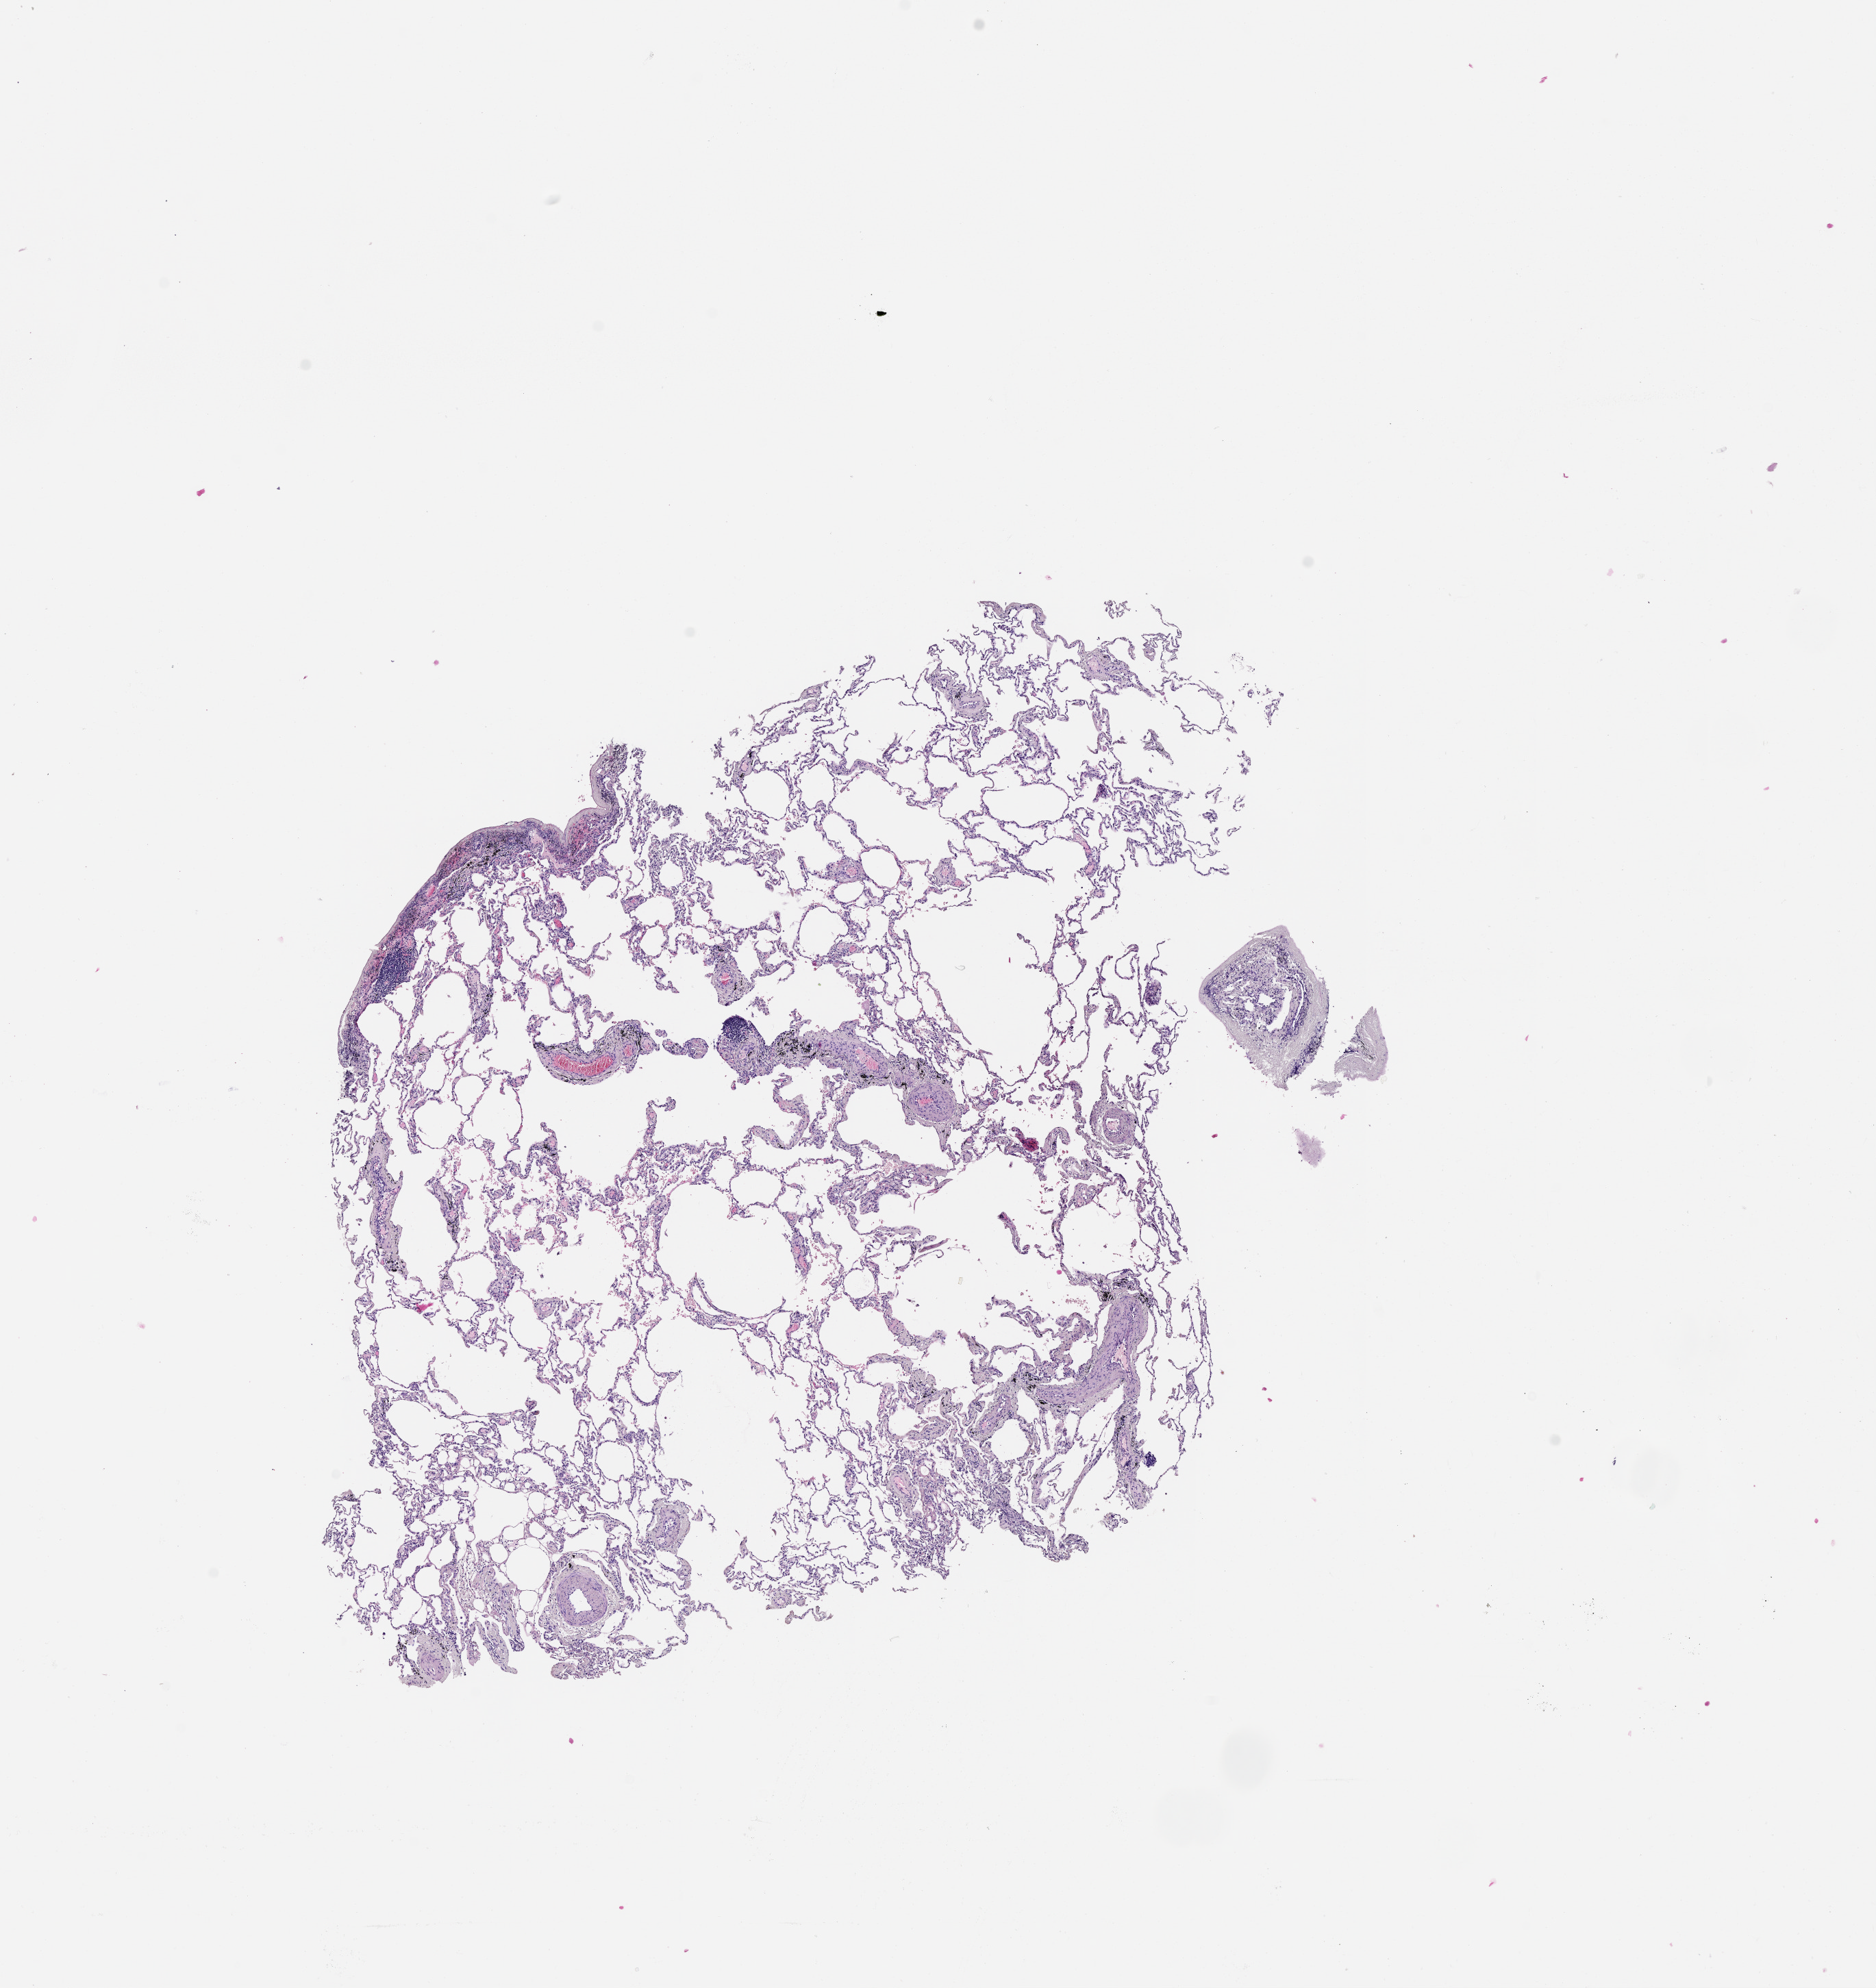
Whole-slide histology image, H&E — a low-resolution overview of the entire scanned area, about 11.0 x 11.7 mm; normal (non-tumour) tissue sample, lung. 60-year-old male patient.
This section: normal (non-tumour) tissue from the same patient. Patient diagnosis (cohort enrolment): squamous cell carcinoma (lung).